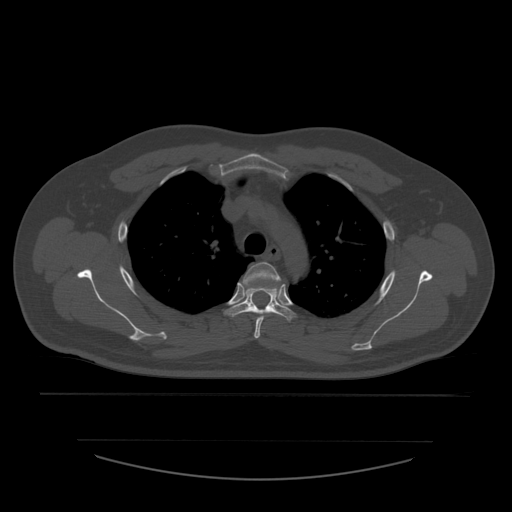
CT including the spine, one axial slice. Position 423 of 532 along the scan axis. Reconstruction kernel STANDARD. Bone window (W 1800 / L 400 HU). 1.25 mm slice thickness. 512 × 512 image matrix, field of view 441 × 441 mm. Patient age 44 years. From the clinical record (not read from this slice): primary cancer: soft tissue sarcoma.
Structures marked on this image (semi-automatically segmented with operator editing):
- T3 vertebra: bounding box <241,262,283,339> (left, top, right, bottom; pixels)
- T4 vertebra: <225,287,294,322>